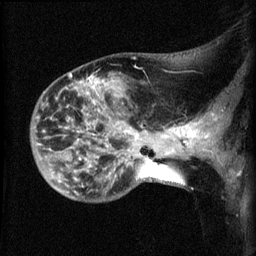
Breast MRI (dynamic contrast-enhanced), one sagittal slice; position 19 of 60 along the scan axis; dynamic contrast-enhanced series, image 2 of 3 at this slice position (ordered by acquisition); 1.5 T; TE 4.2 ms, TR 8.2 ms; 2.1 mm slice thickness; 256 × 256 image matrix. Patient: female, 50 years.
Annotated regions visible in this slice (semi-automatically segmented with operator editing):
- analysis volume of interest (the breast-tissue region the enhancement analysis was run in; not a lesion): bounding box [x1, y1, x2, y2] px = [38, 77, 169, 202]
- tumour enhancement mask (voxels above the 70 % enhancement threshold inside the analysis volume of interest): [86, 78, 166, 137]